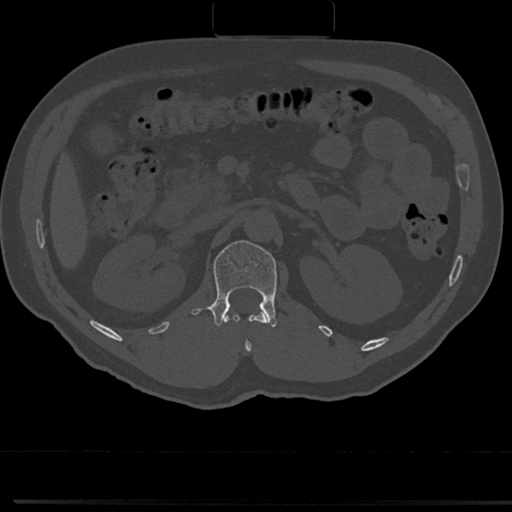
CT including the spine, one axial slice. Position 99 of 817 along the scan axis. Reconstruction kernel Br40s/3. Bone window (W 1800 / L 400 HU). 512 × 512 image matrix, field of view 355 × 355 mm. Patient: male, 61 years. Case-level facts recorded for this patient, not image findings: primary cancer: prostate.
Outlined on this slice (semi-automatic segmentation, software-assisted and operator-edited):
- L1 vertebra: bounding box (x1, y1, x2, y2) in pixels: (191, 240, 278, 327)
- T12 vertebra: (247, 313, 267, 349)